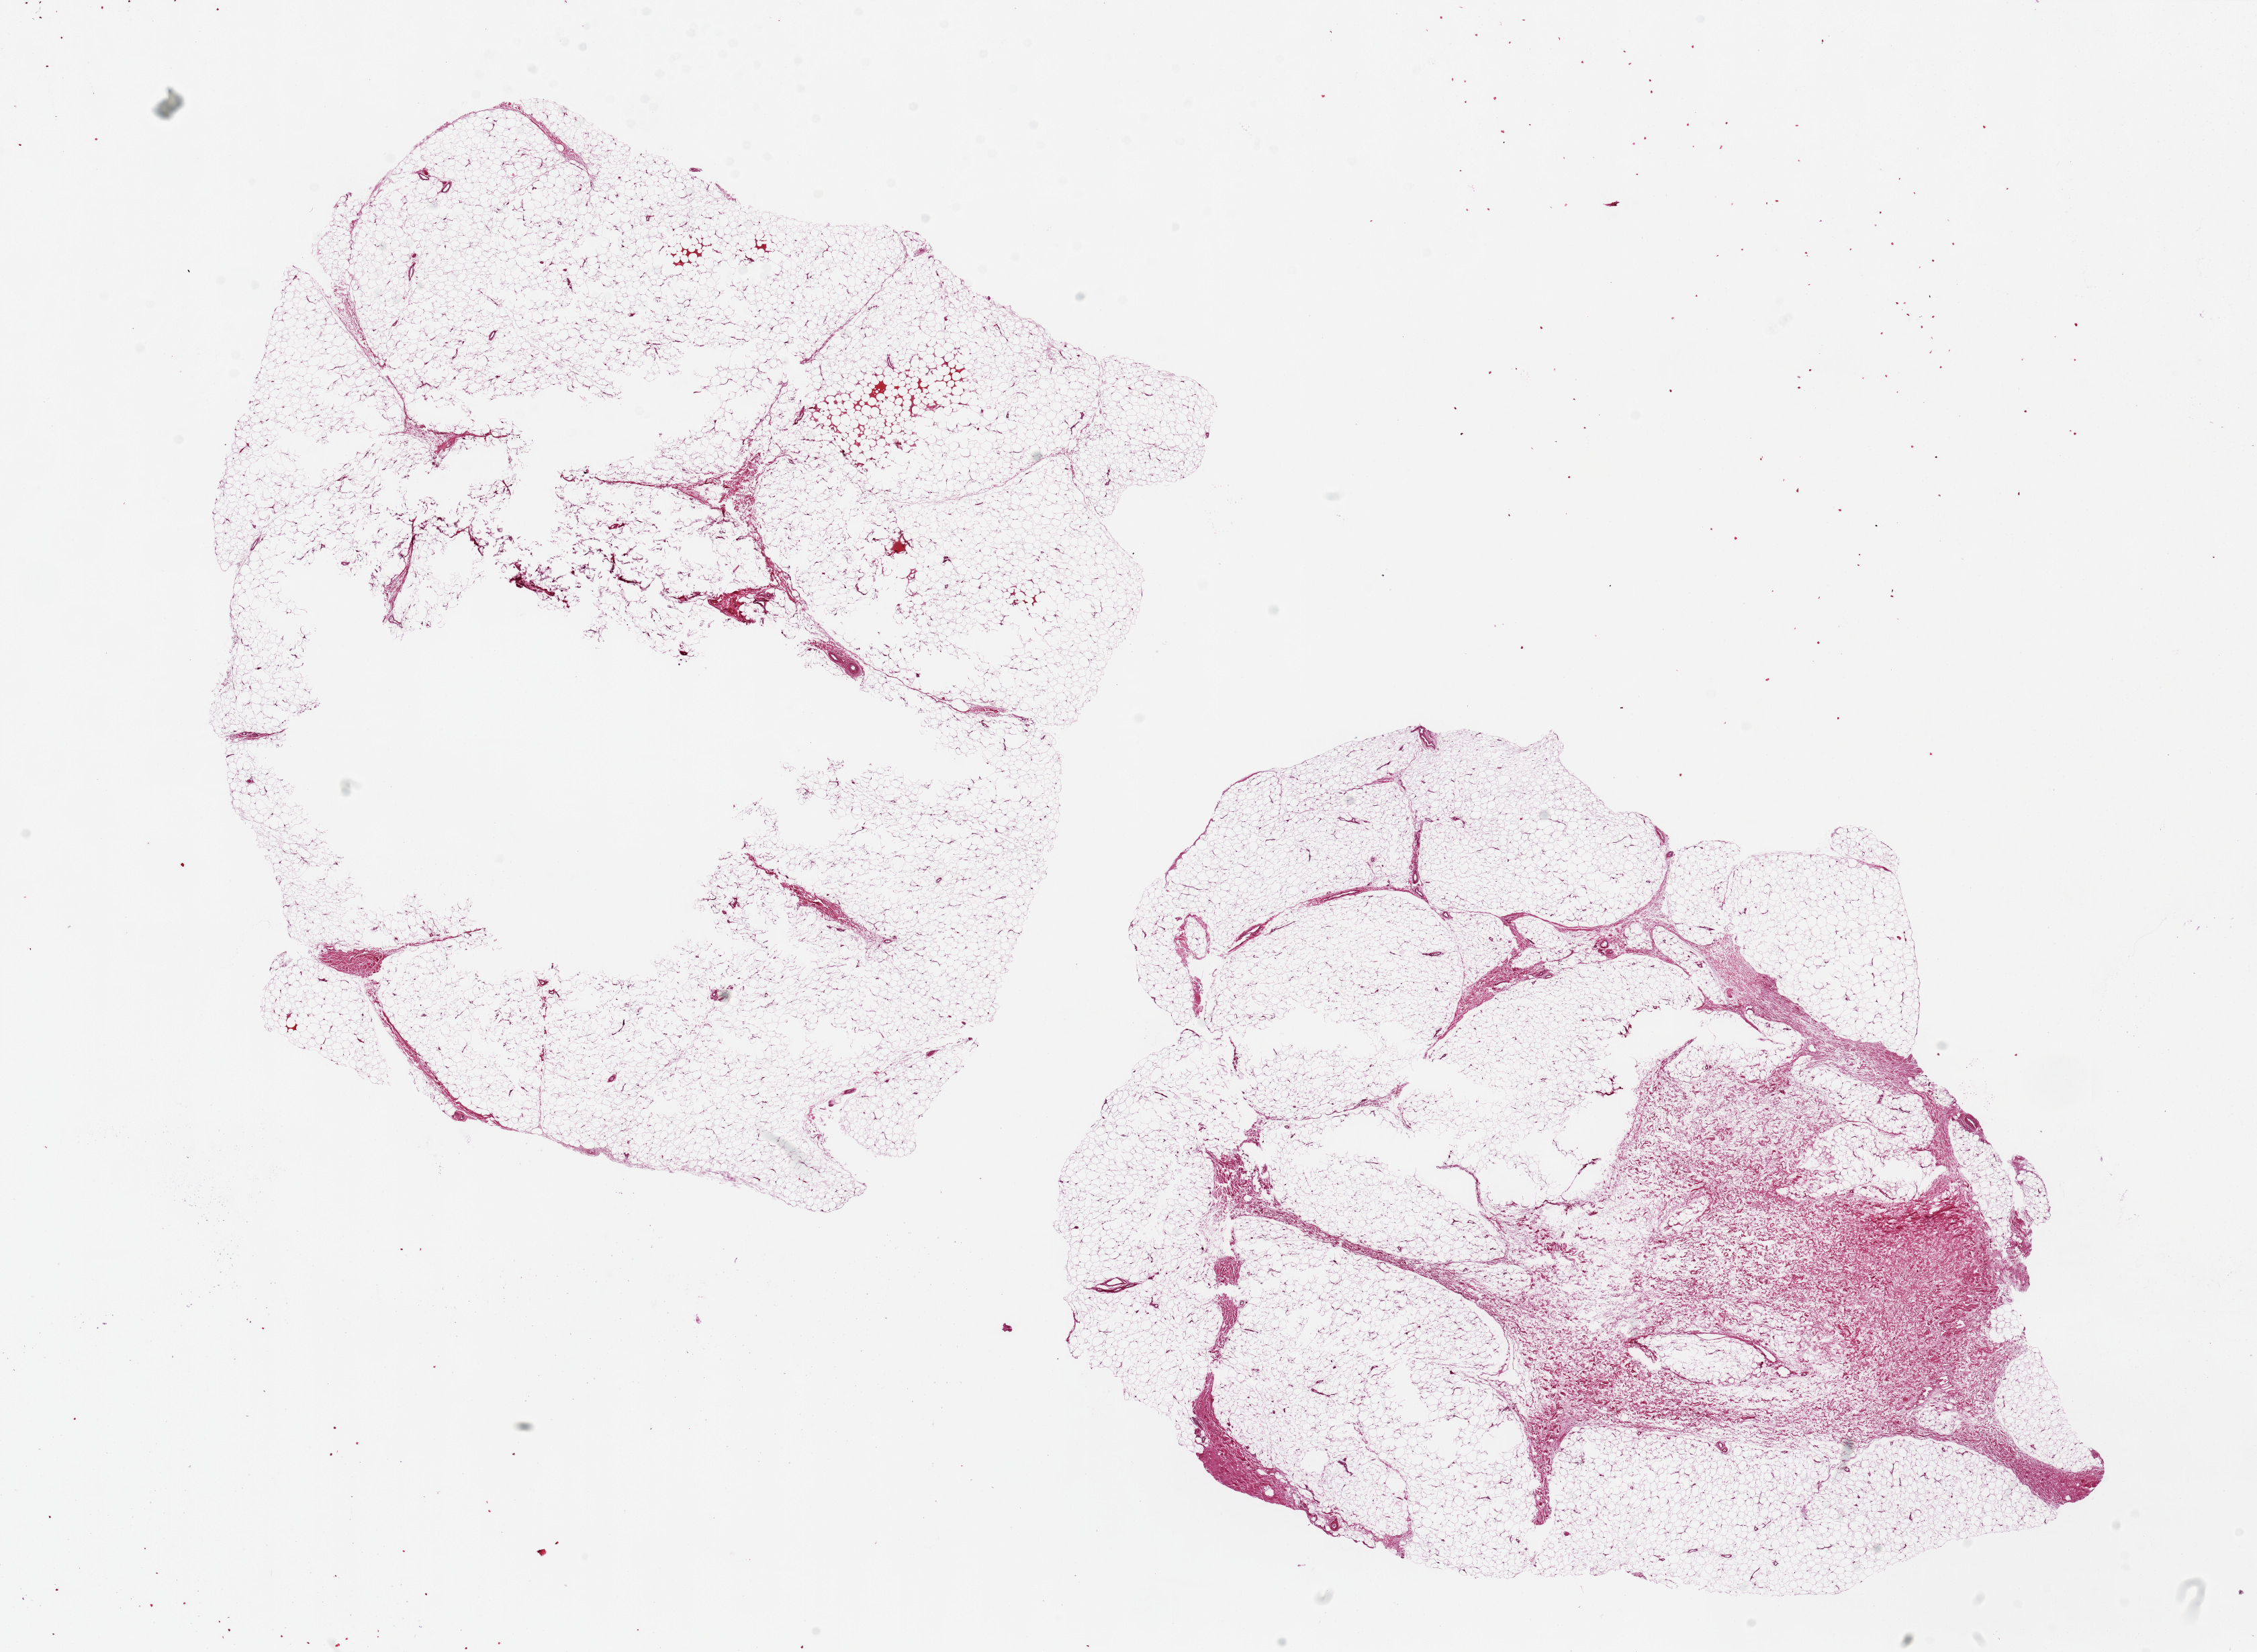
Whole-slide image, haematoxylin and eosin stain, a low-resolution overview of the entire scanned area, about 26.6 x 19.5 mm. PAXgene-fixed paraffin-embedded (PFPE) section. Target tissue: adipose tissue. Tissue donor sample. Donor sex: male.
Pathologist's review note for this sample: 2 pieces, 11x10 & 12x9mm; ~30% central defect in one; 10% in other.